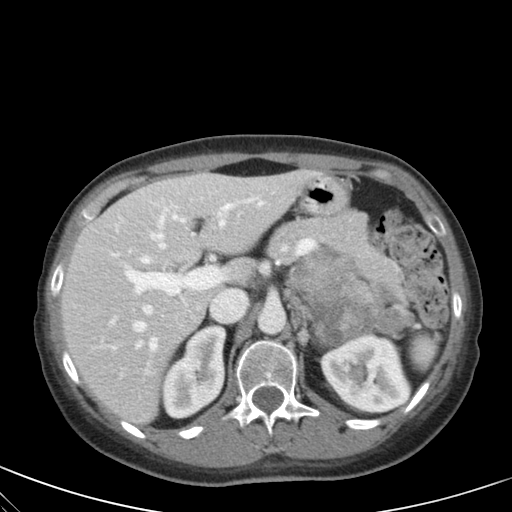
Contrast-enhanced abdominal CT, one axial slice. Position 37 of 59 along the scan axis. 120 kVp. Intravenous contrast given. Soft-tissue window (W 400 / L 40 HU). 4 mm slice thickness. 512 × 512 image matrix. Female patient, age 28 years. From the clinical record (not read from this slice): diagnosis: adrenocortical carcinoma; tumour side: left adrenal; tumour size at pathology: 7 cm; Ki-67 index: 40 %; stage (as recorded): 4.
Outlined on this slice (semi-automatically segmented with operator editing):
- mass: bounding box [x1, y1, x2, y2] px = [291, 250, 415, 349]